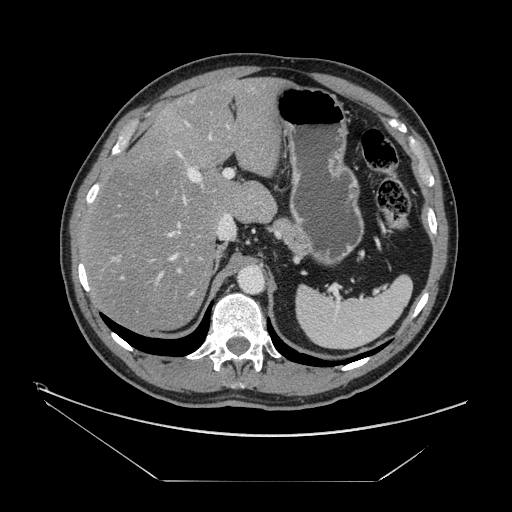
Contrast-enhanced abdominal CT, one axial slice; slice 99 of 161 in the series (ordered by position); reconstruction kernel STANDARD; 120 kVp; intravenous contrast given; soft-tissue window (W 400 / L 40 HU); 2.5 mm slice thickness; 512 × 512 image matrix, field of view 440 × 440 mm. Male patient, age 65 years. From the clinical record (not read from this slice): diagnosis: colorectal cancer liver metastases, imaged before liver resection; multiple liver metastases: yes; largest metastasis: 4.2 cm; chemotherapy before resection: yes.
Outlined on this slice (manually delineated by an expert):
- hepatic veins: box from (x=120, y=123) to (x=211, y=280) px
- liver: (x=83, y=79)–(x=282, y=329)
- planned liver remnant (the part of the liver to remain after resection): (x=83, y=79)–(x=282, y=330)
- portal vein (with intrahepatic branches): (x=111, y=88)–(x=253, y=290)